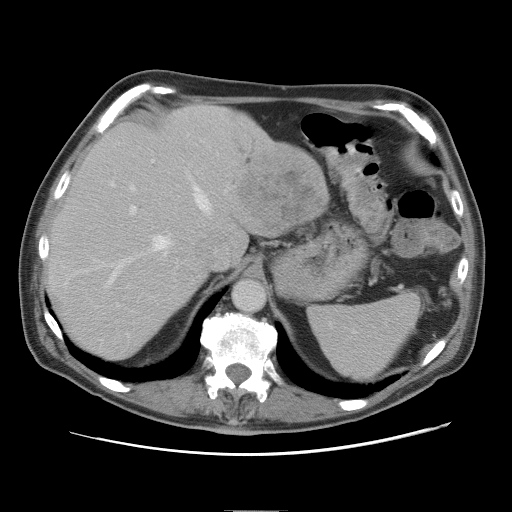
Contrast-enhanced abdominal CT, one axial slice; slice 59 of 89 in the series (ordered by position); 120 kVp; intravenous contrast given; soft-tissue window (W 400 / L 40 HU); 5 mm slice thickness; 512 × 512 image matrix. Male patient, age 69 years. Case-level facts recorded for this patient, not image findings: diagnosis: colorectal cancer liver metastases, imaged before liver resection.
Structures marked on this image (outlined manually by an expert reader):
- hepatic veins: bounding box (x1, y1, x2, y2) in pixels: (109, 170, 212, 284)
- liver: (49, 104, 328, 357)
- planned liver remnant (the part of the liver to remain after resection): (49, 105, 245, 358)
- portal vein (with intrahepatic branches): (130, 140, 209, 214)
- liver metastasis: (239, 166, 319, 228)